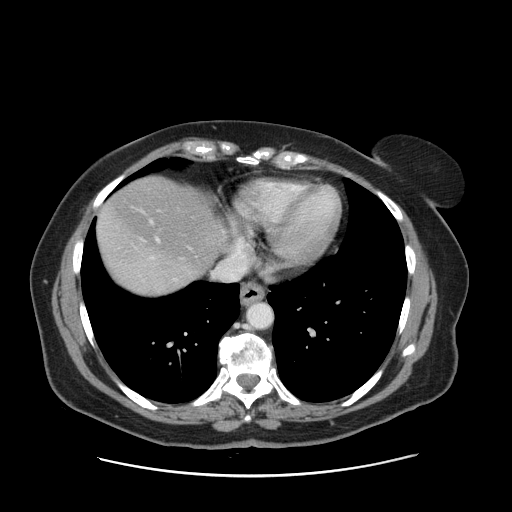
Contrast-enhanced abdominal CT, one axial slice. Slice 141 of 161 in the series (ordered by position). 120 kVp. Intravenous contrast given. Soft-tissue window (W 400 / L 40 HU). 2.5 mm slice thickness. 512 × 512 image matrix. Female patient, age 62 years. Case-level facts recorded for this patient, not image findings: diagnosis: colorectal cancer liver metastases, imaged before liver resection; multiple liver metastases: no; largest metastasis: 2.5 cm; disease in both lobes: no.
Structures marked on this image (manually delineated by an expert):
- hepatic veins: bounding box (x1, y1, x2, y2) in pixels: (141, 237, 160, 258)
- liver: (98, 177, 220, 296)
- planned liver remnant (the part of the liver to remain after resection): (99, 177, 220, 273)